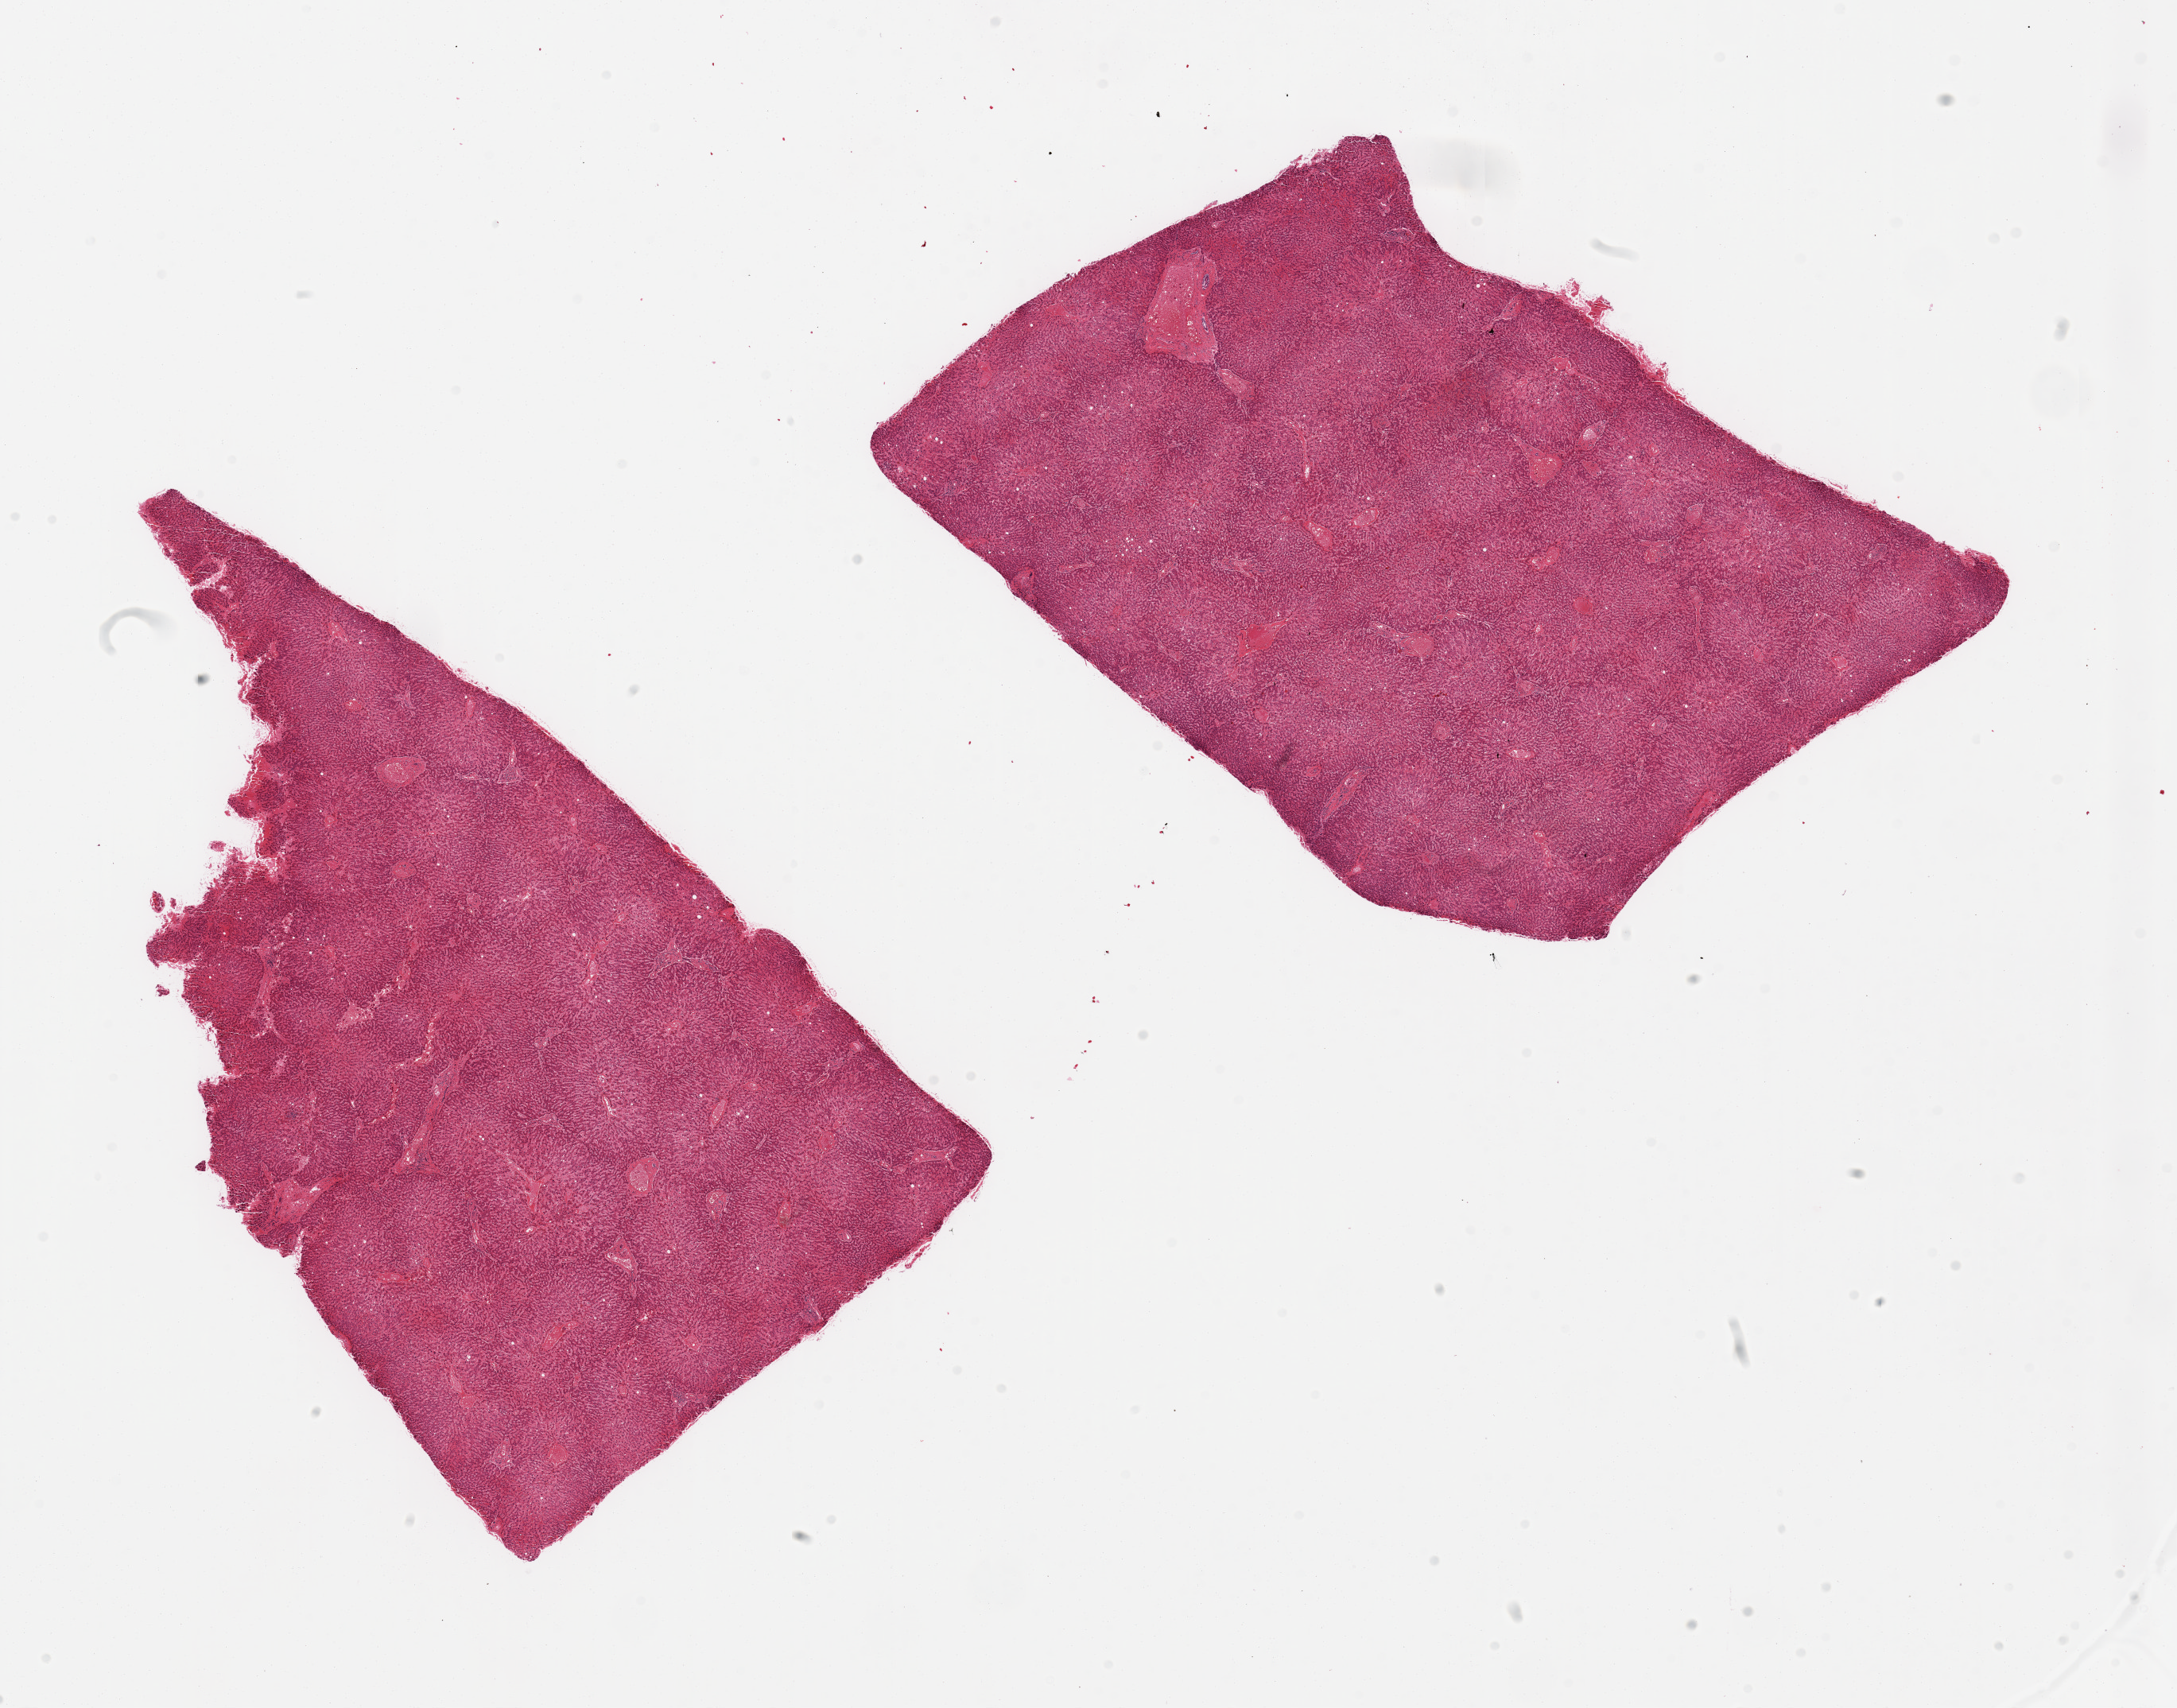
Whole-slide image, H&E stain, a low-resolution overview of the entire scanned area, about 21.7 x 17.0 mm. PAXgene-fixed, paraffin-embedded tissue. Sampled site (target tissue): liver. Donor tissue sample. Male donor.
Pathologist's review note for this sample: 2 pieces.